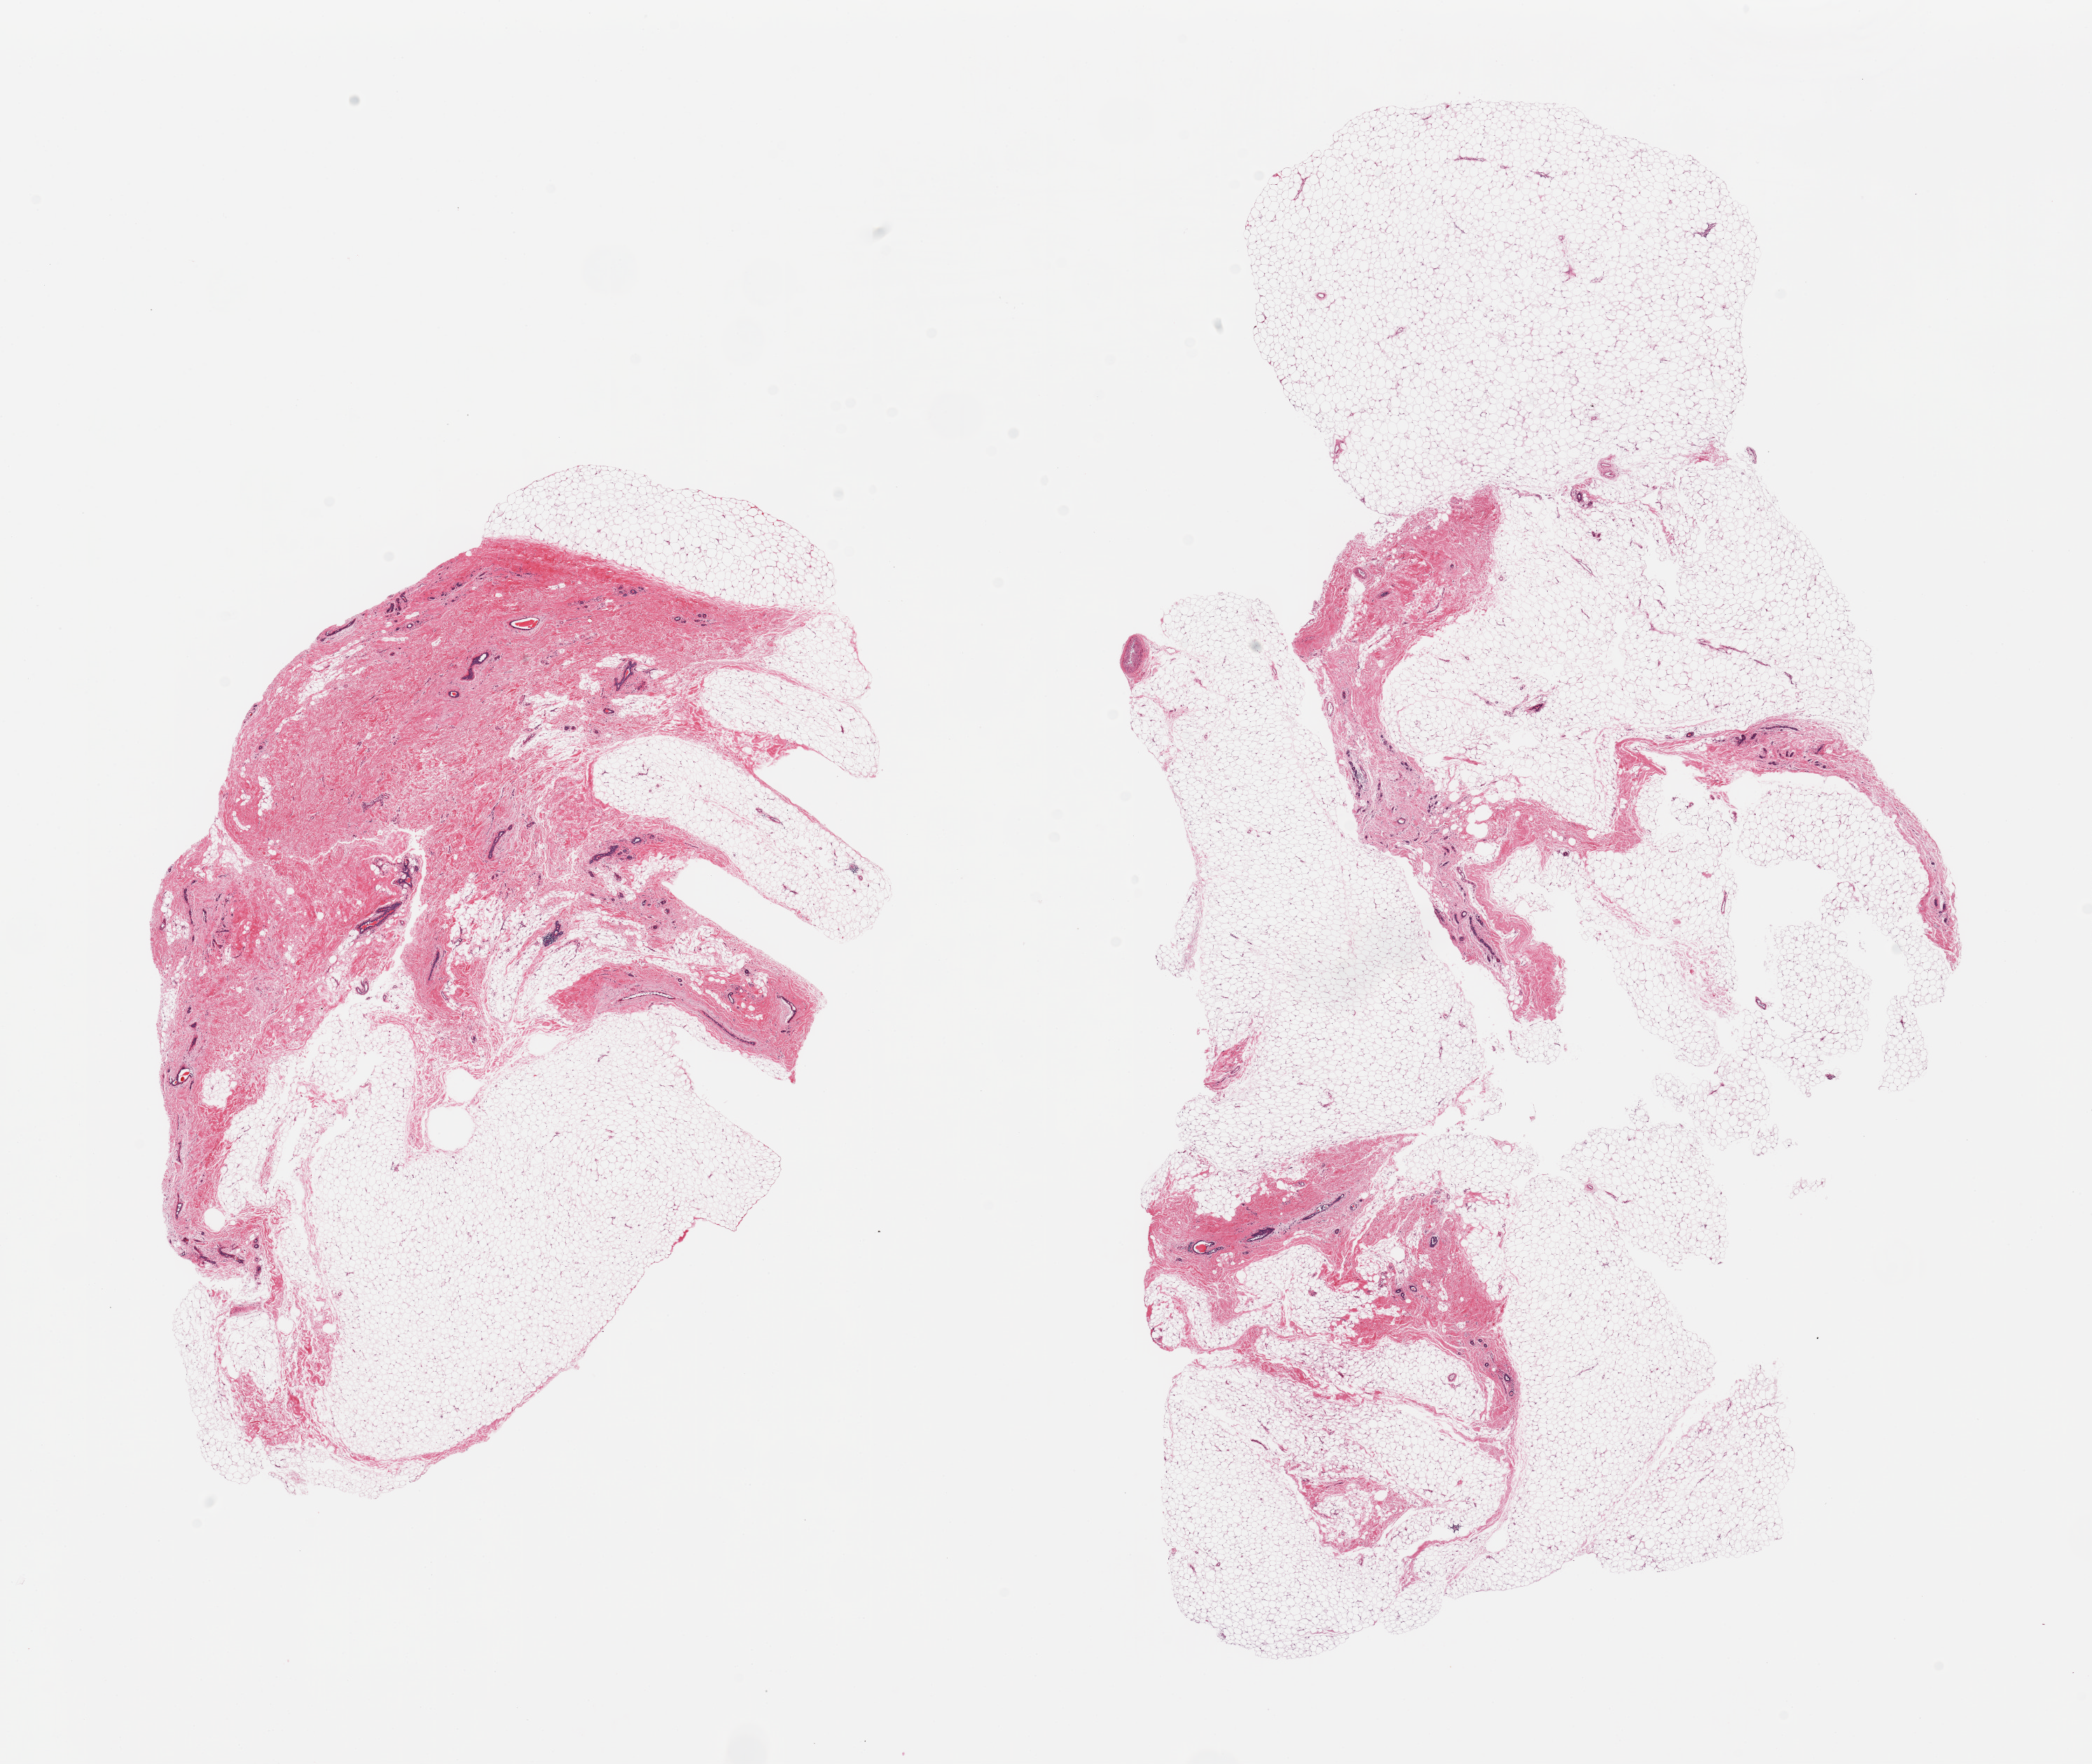
Digitized haematoxylin and eosin-stained section, brightfield, a low-resolution overview of the entire scanned area, about 23.6 x 19.9 mm; PAXgene-fixed paraffin-embedded (PFPE) section; section of breast (target tissue); tissue donor sample. Female donor.
Review note (as recorded): 2 pieces; ducts and atrophic lobules; 50 & 80% fat.